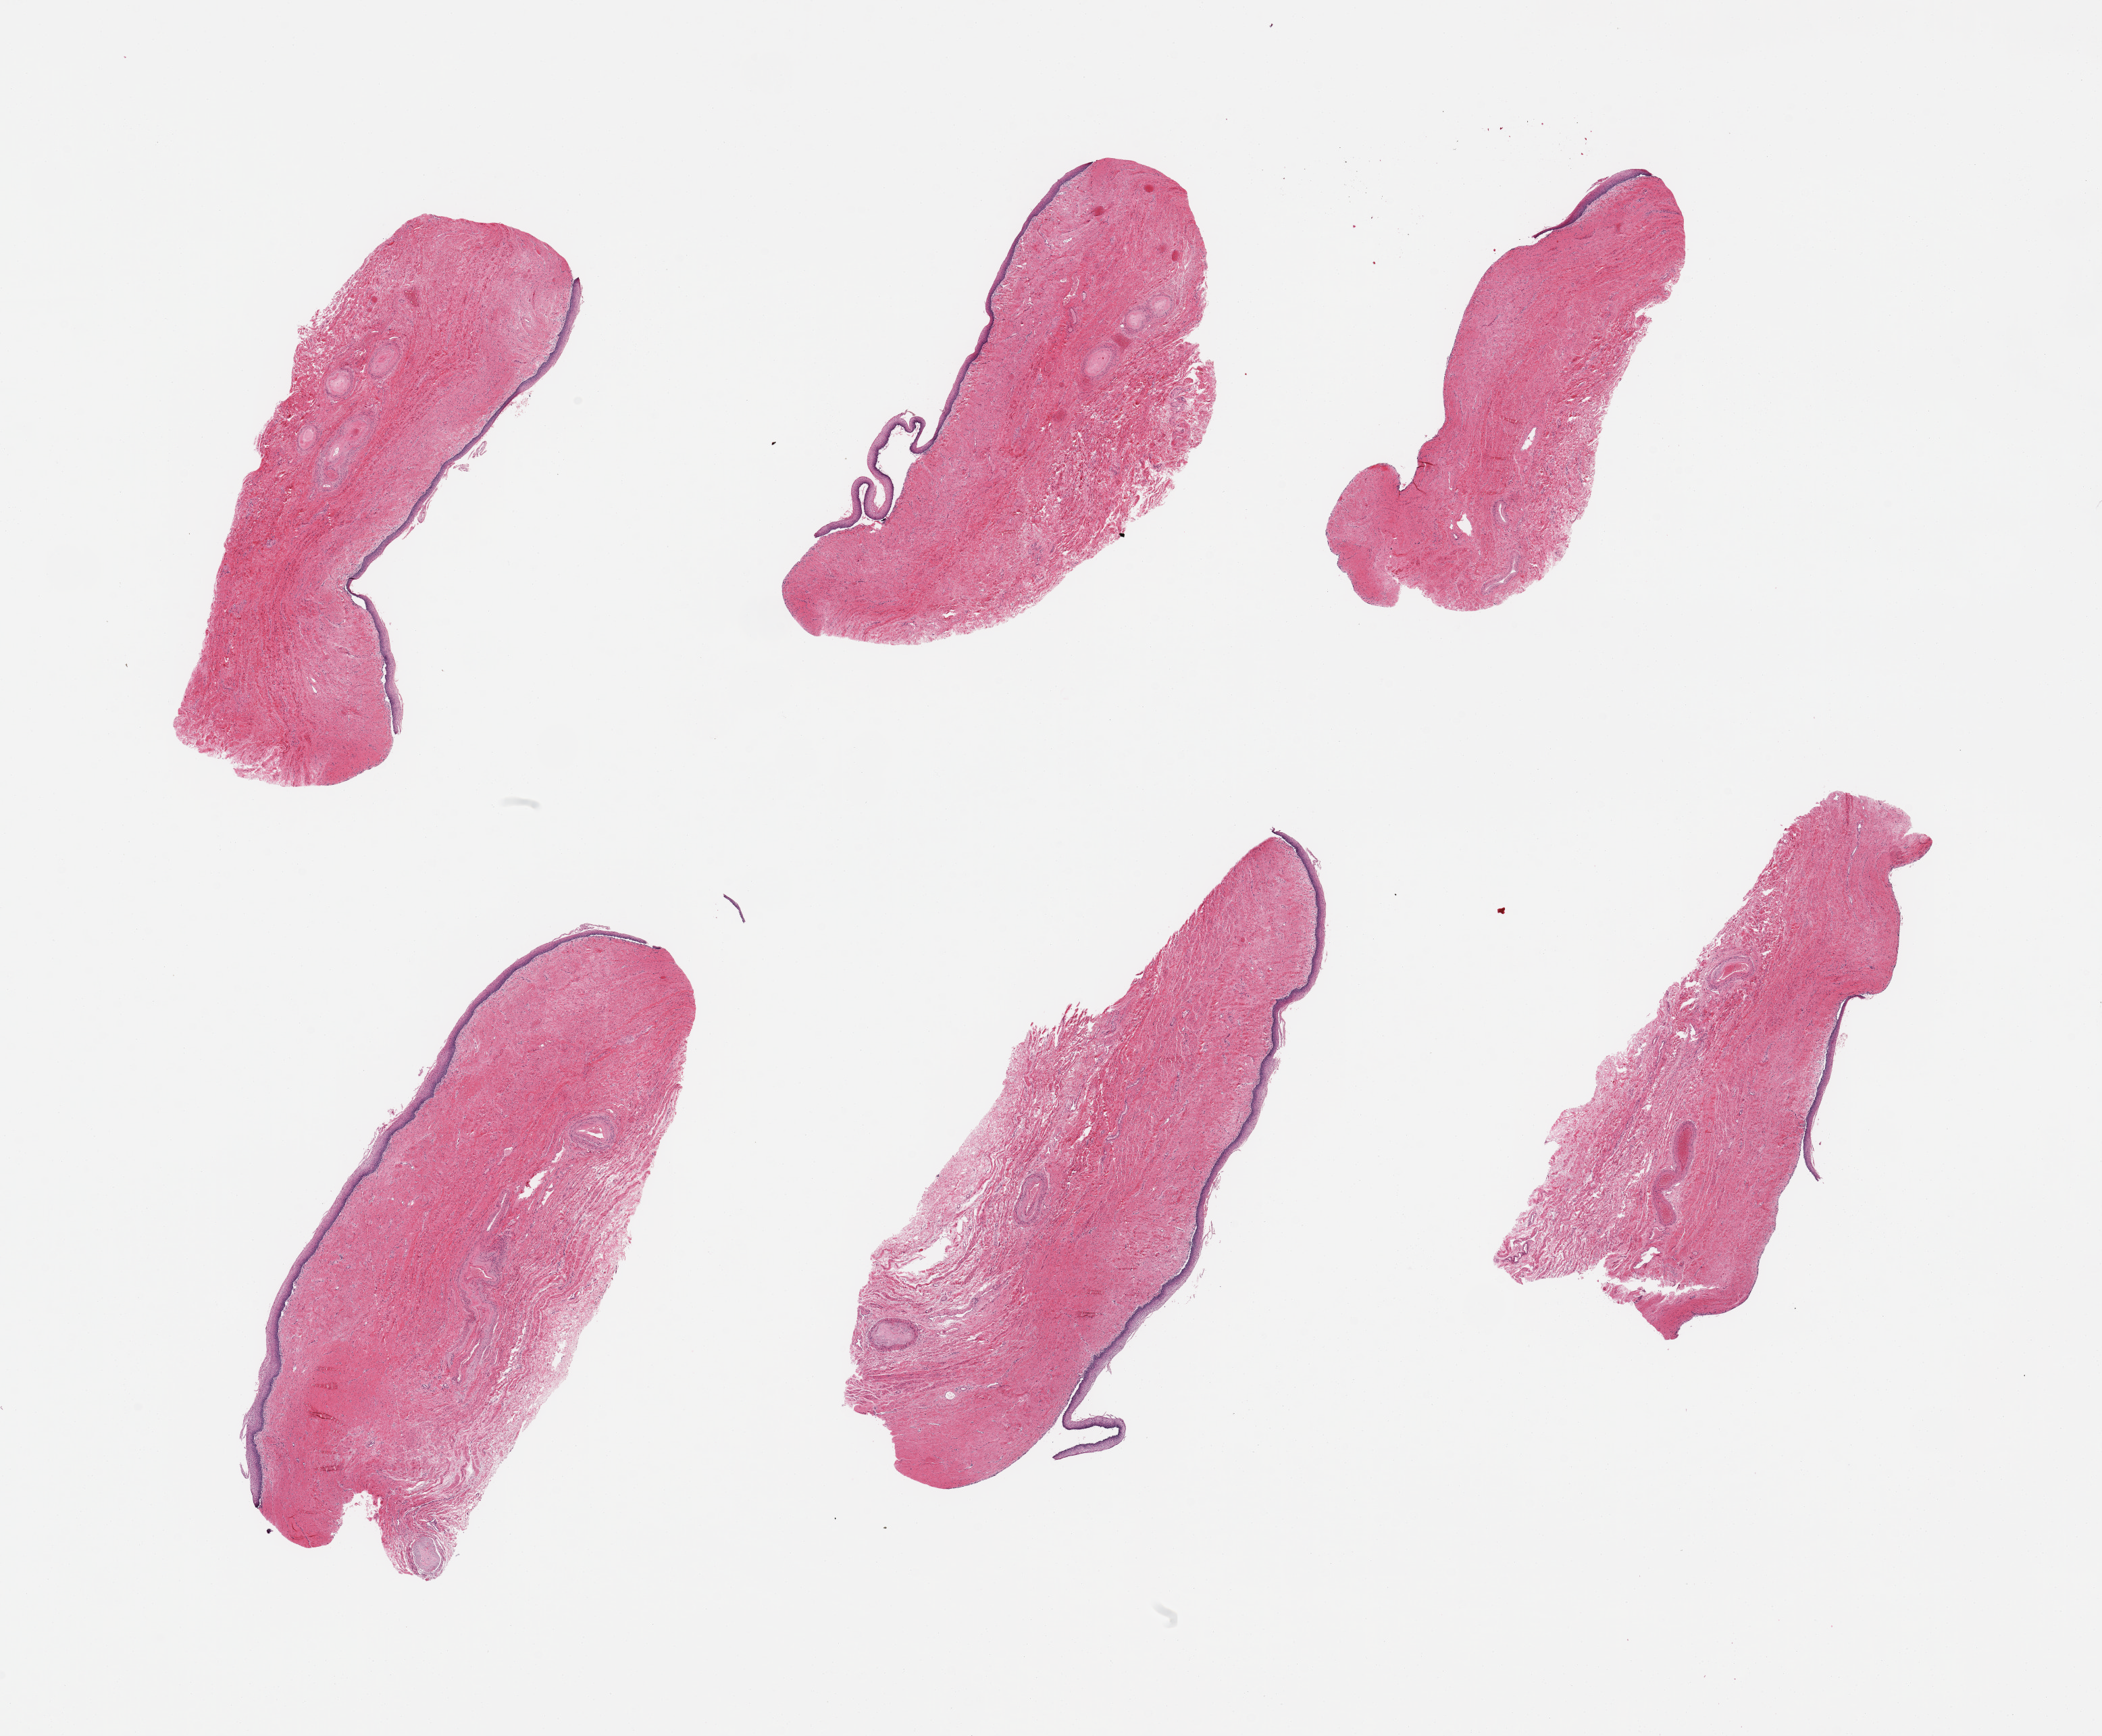
Whole-slide image, haematoxylin and eosin stain — shown as a low-resolution overview of the whole scanned area (about 24.6 x 20.3 mm). PAXgene-fixed, paraffin-embedded tissue. Target tissue: vagina. Tissue donor sample. Donor: female.
Reviewer comment on this tissue sample: 6 pieces.